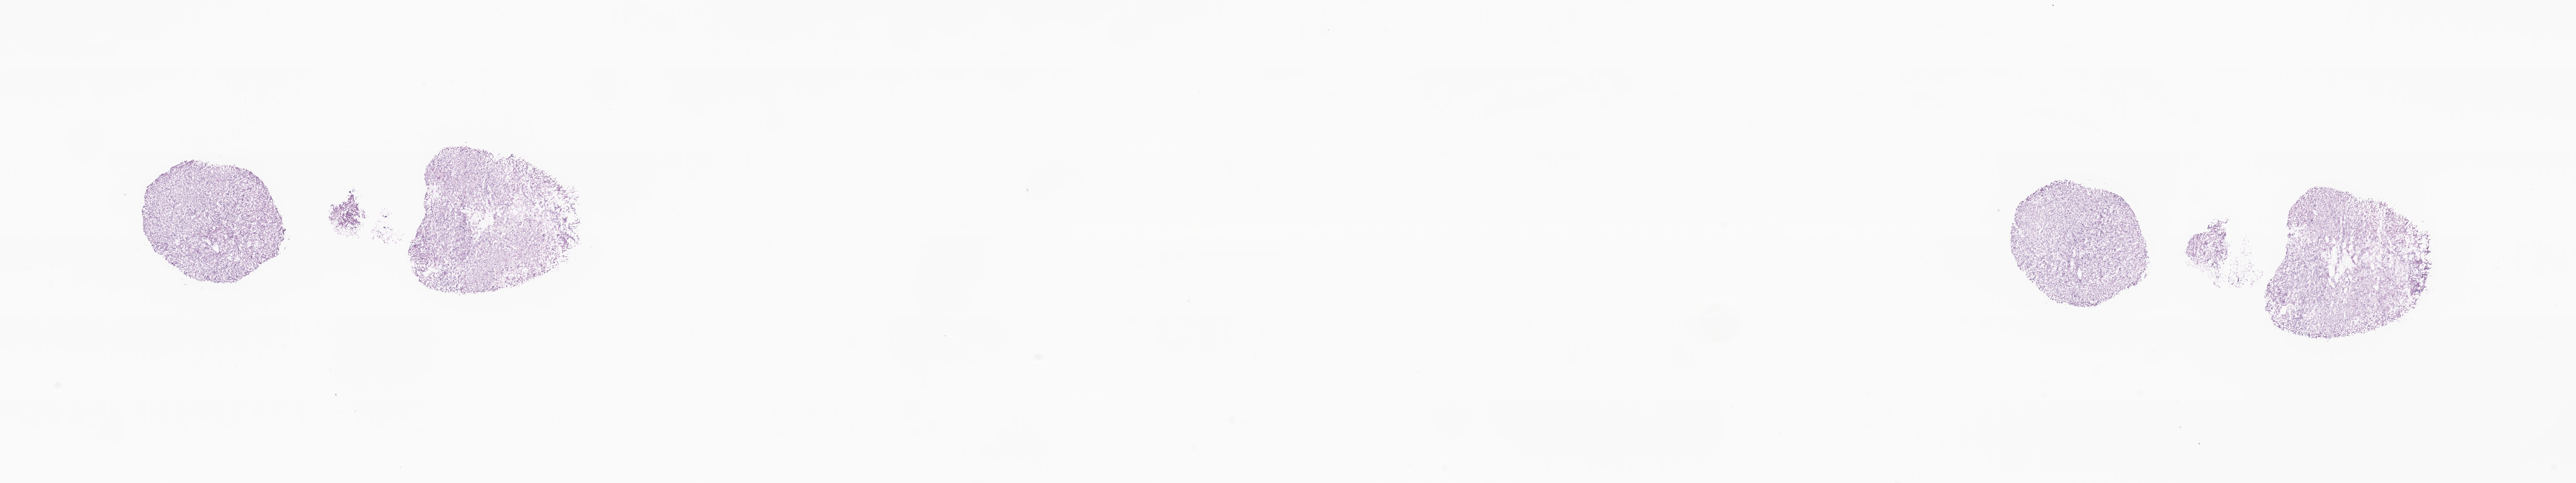
Whole-slide image, H&E stain, shown as a low-resolution overview of the whole scanned area (about 33.1 x 6.2 mm); cryosection; metastatic tumor tissue, resected from connective, subcutaneous and other soft tissues. Patient: female, age at initial diagnosis 45 years. Slide review estimates, as recorded: tumor cells 90%, tumor nuclei 90%, stromal cells 10%, necrosis 0%, normal cells 0%. Infiltration values recorded for this section: lymphocyte infiltration 0%, monocyte infiltration 0%, neutrophil infiltration 0%.
Patient diagnosis (primary): Leiomyosarcoma, NOS.